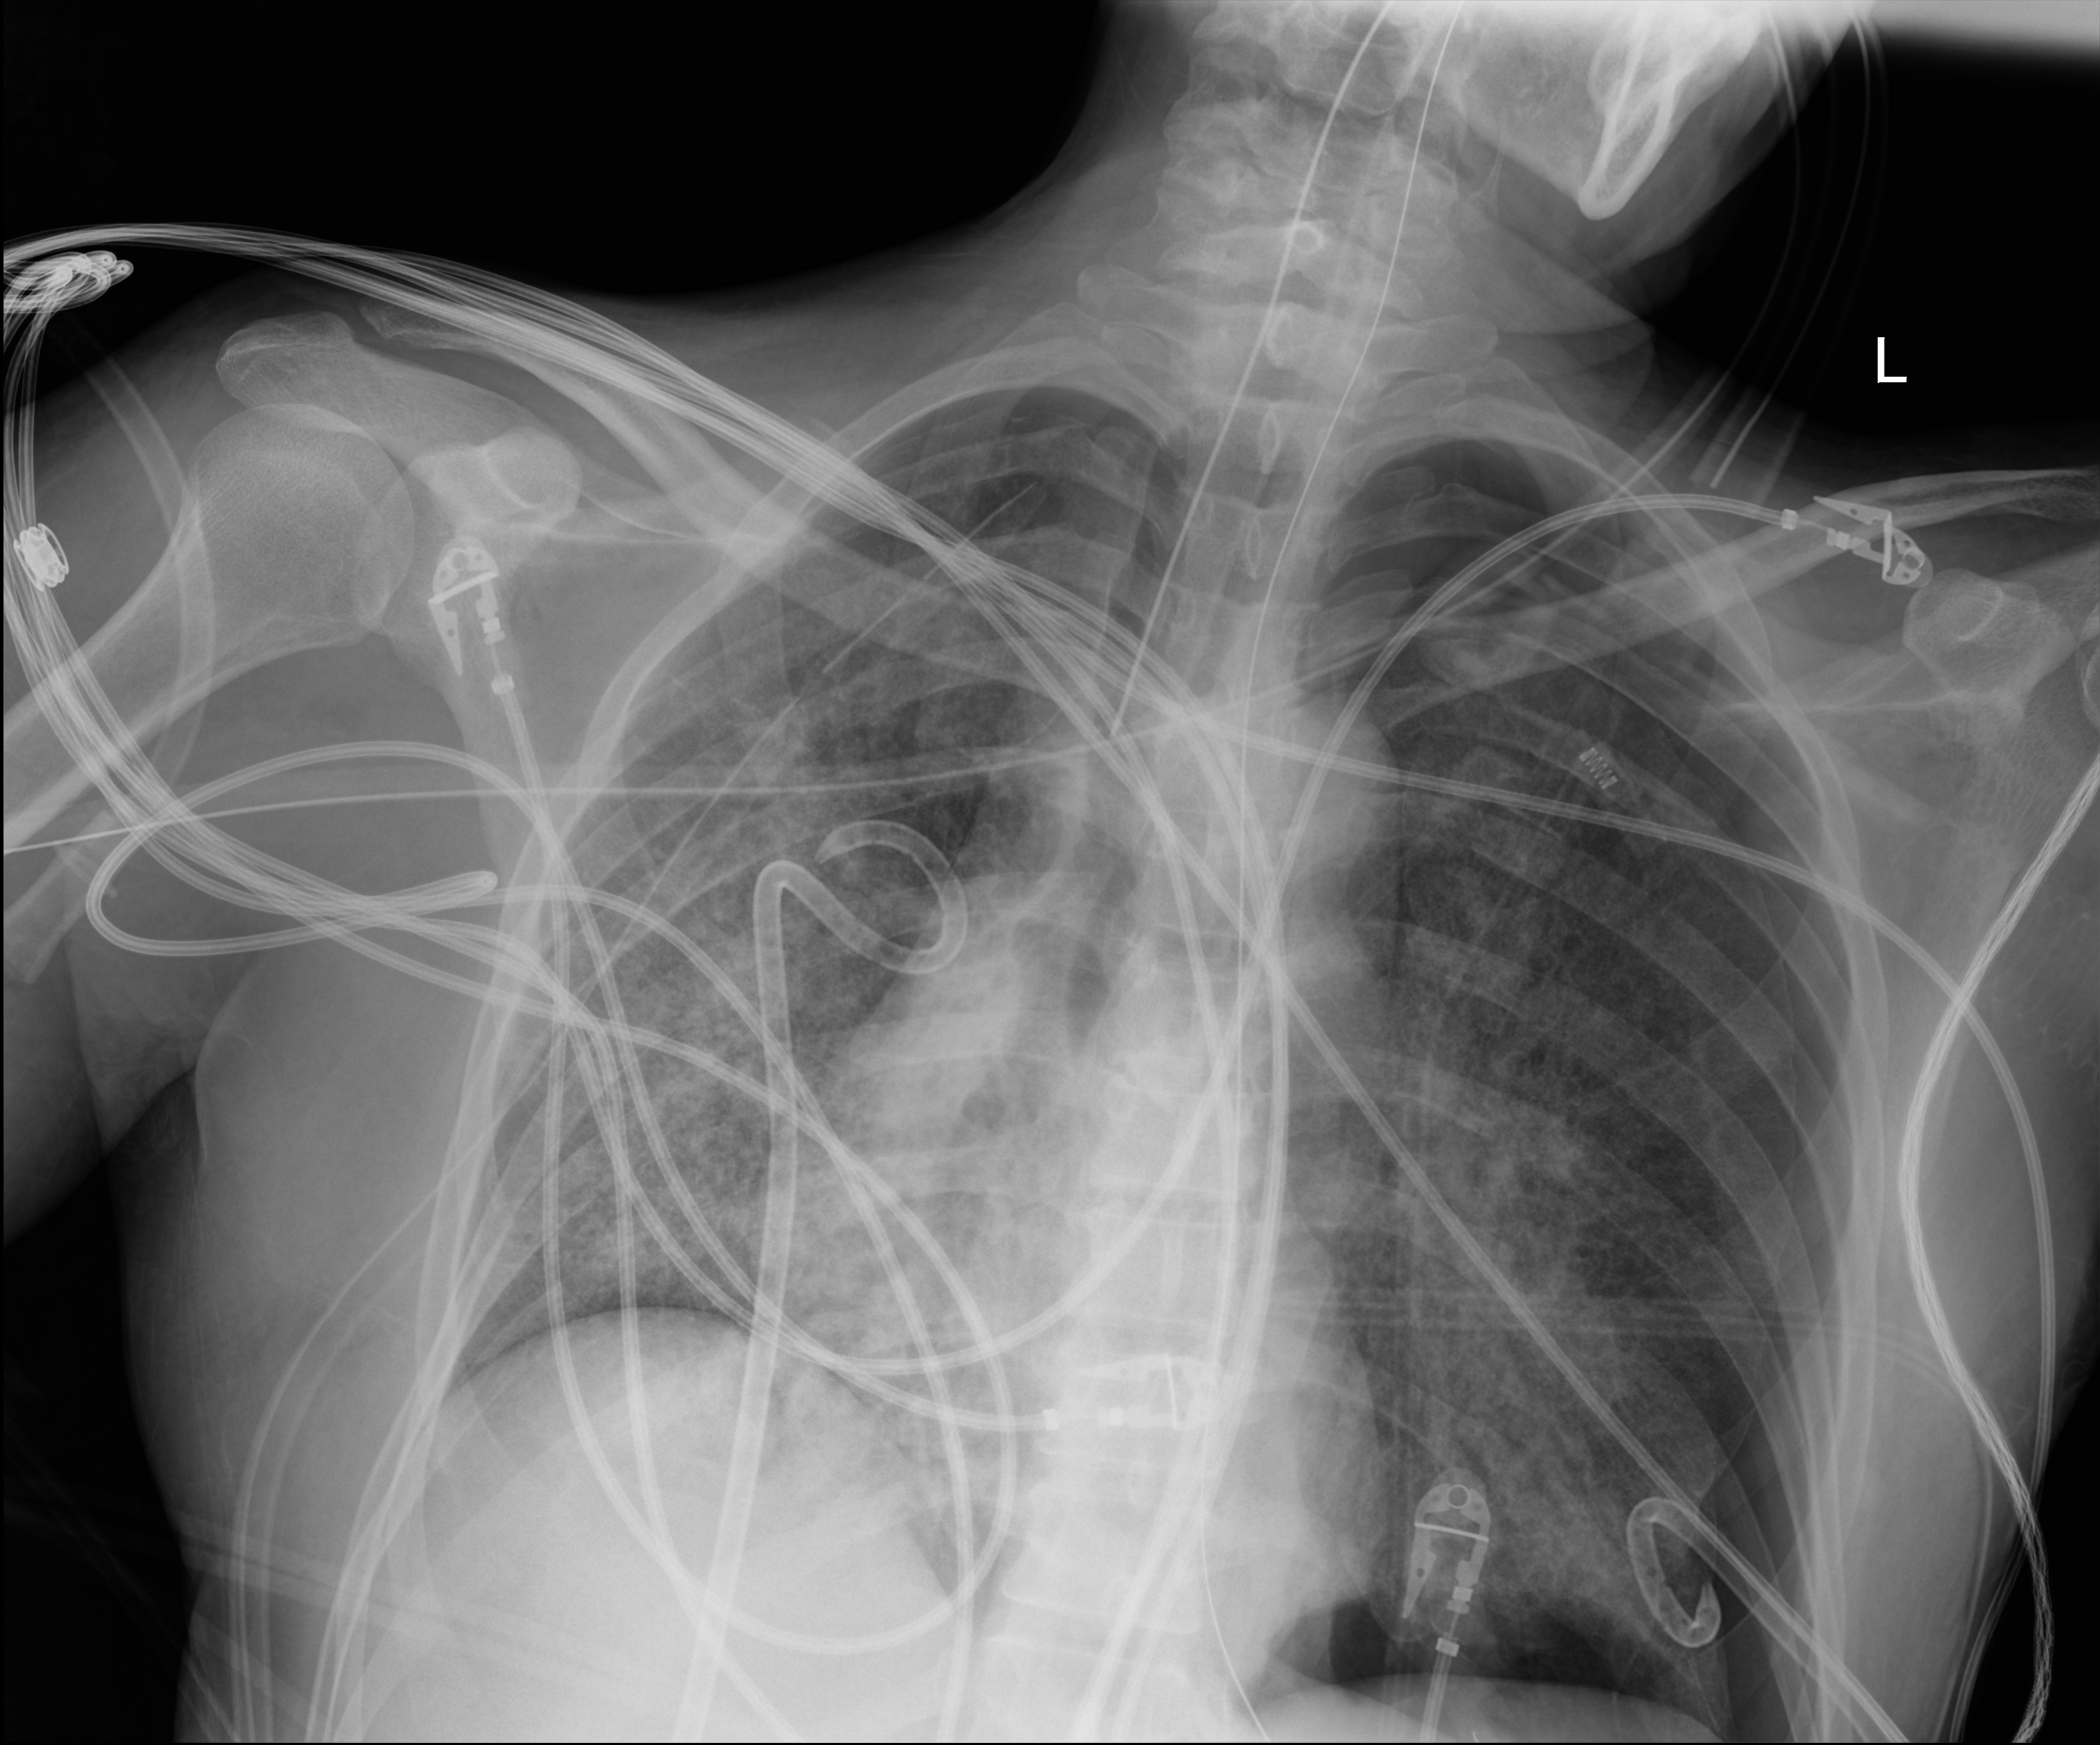
Chest radiograph. Patient hospitalised with COVID-19, aged 18–59 years.
Hospital-stay facts (about this admission, not read from this image; timing relative to this image not recorded): hypertension (admission record): no; mechanically ventilated during this hospital stay: yes; admitted to intensive care during this hospital stay: yes.